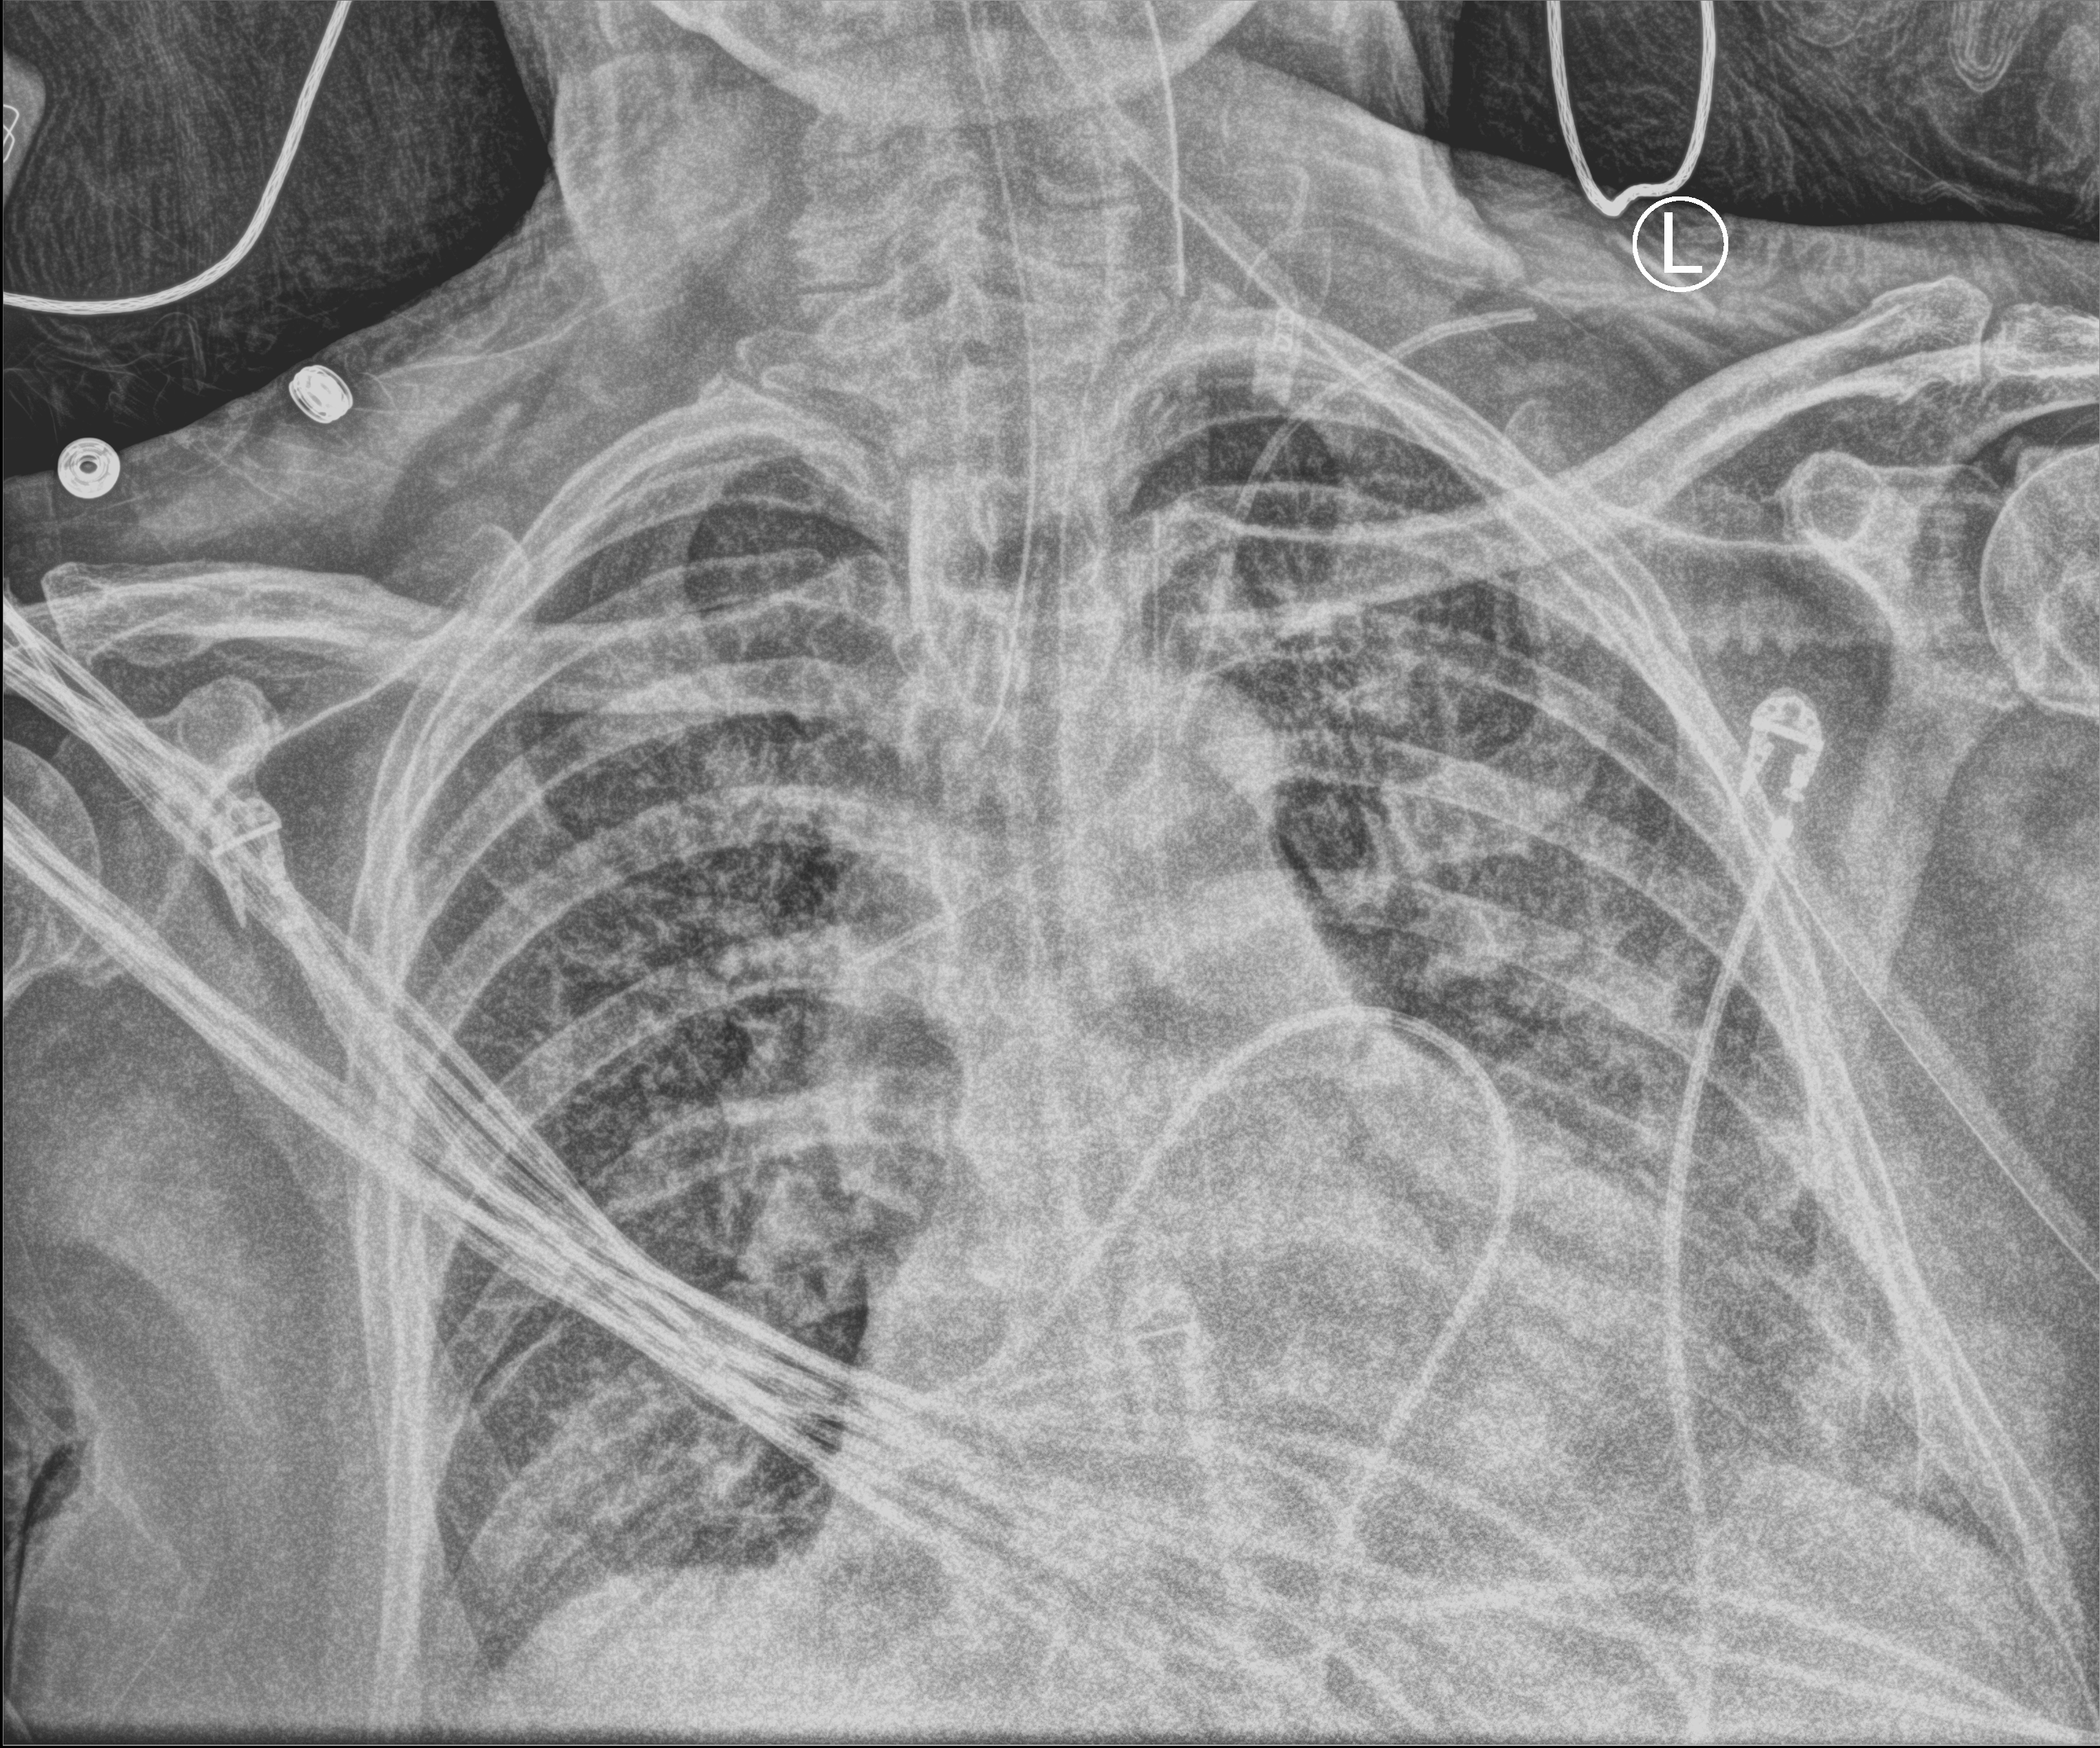
Chest X-ray (portable). Patient hospitalised with COVID-19; male, aged 75–90 years.
From the hospital-stay record, not from the radiograph (when in the stay this image was taken is not recorded):
- admitted to intensive care during this hospital stay: yes
- mechanically ventilated during this hospital stay: yes